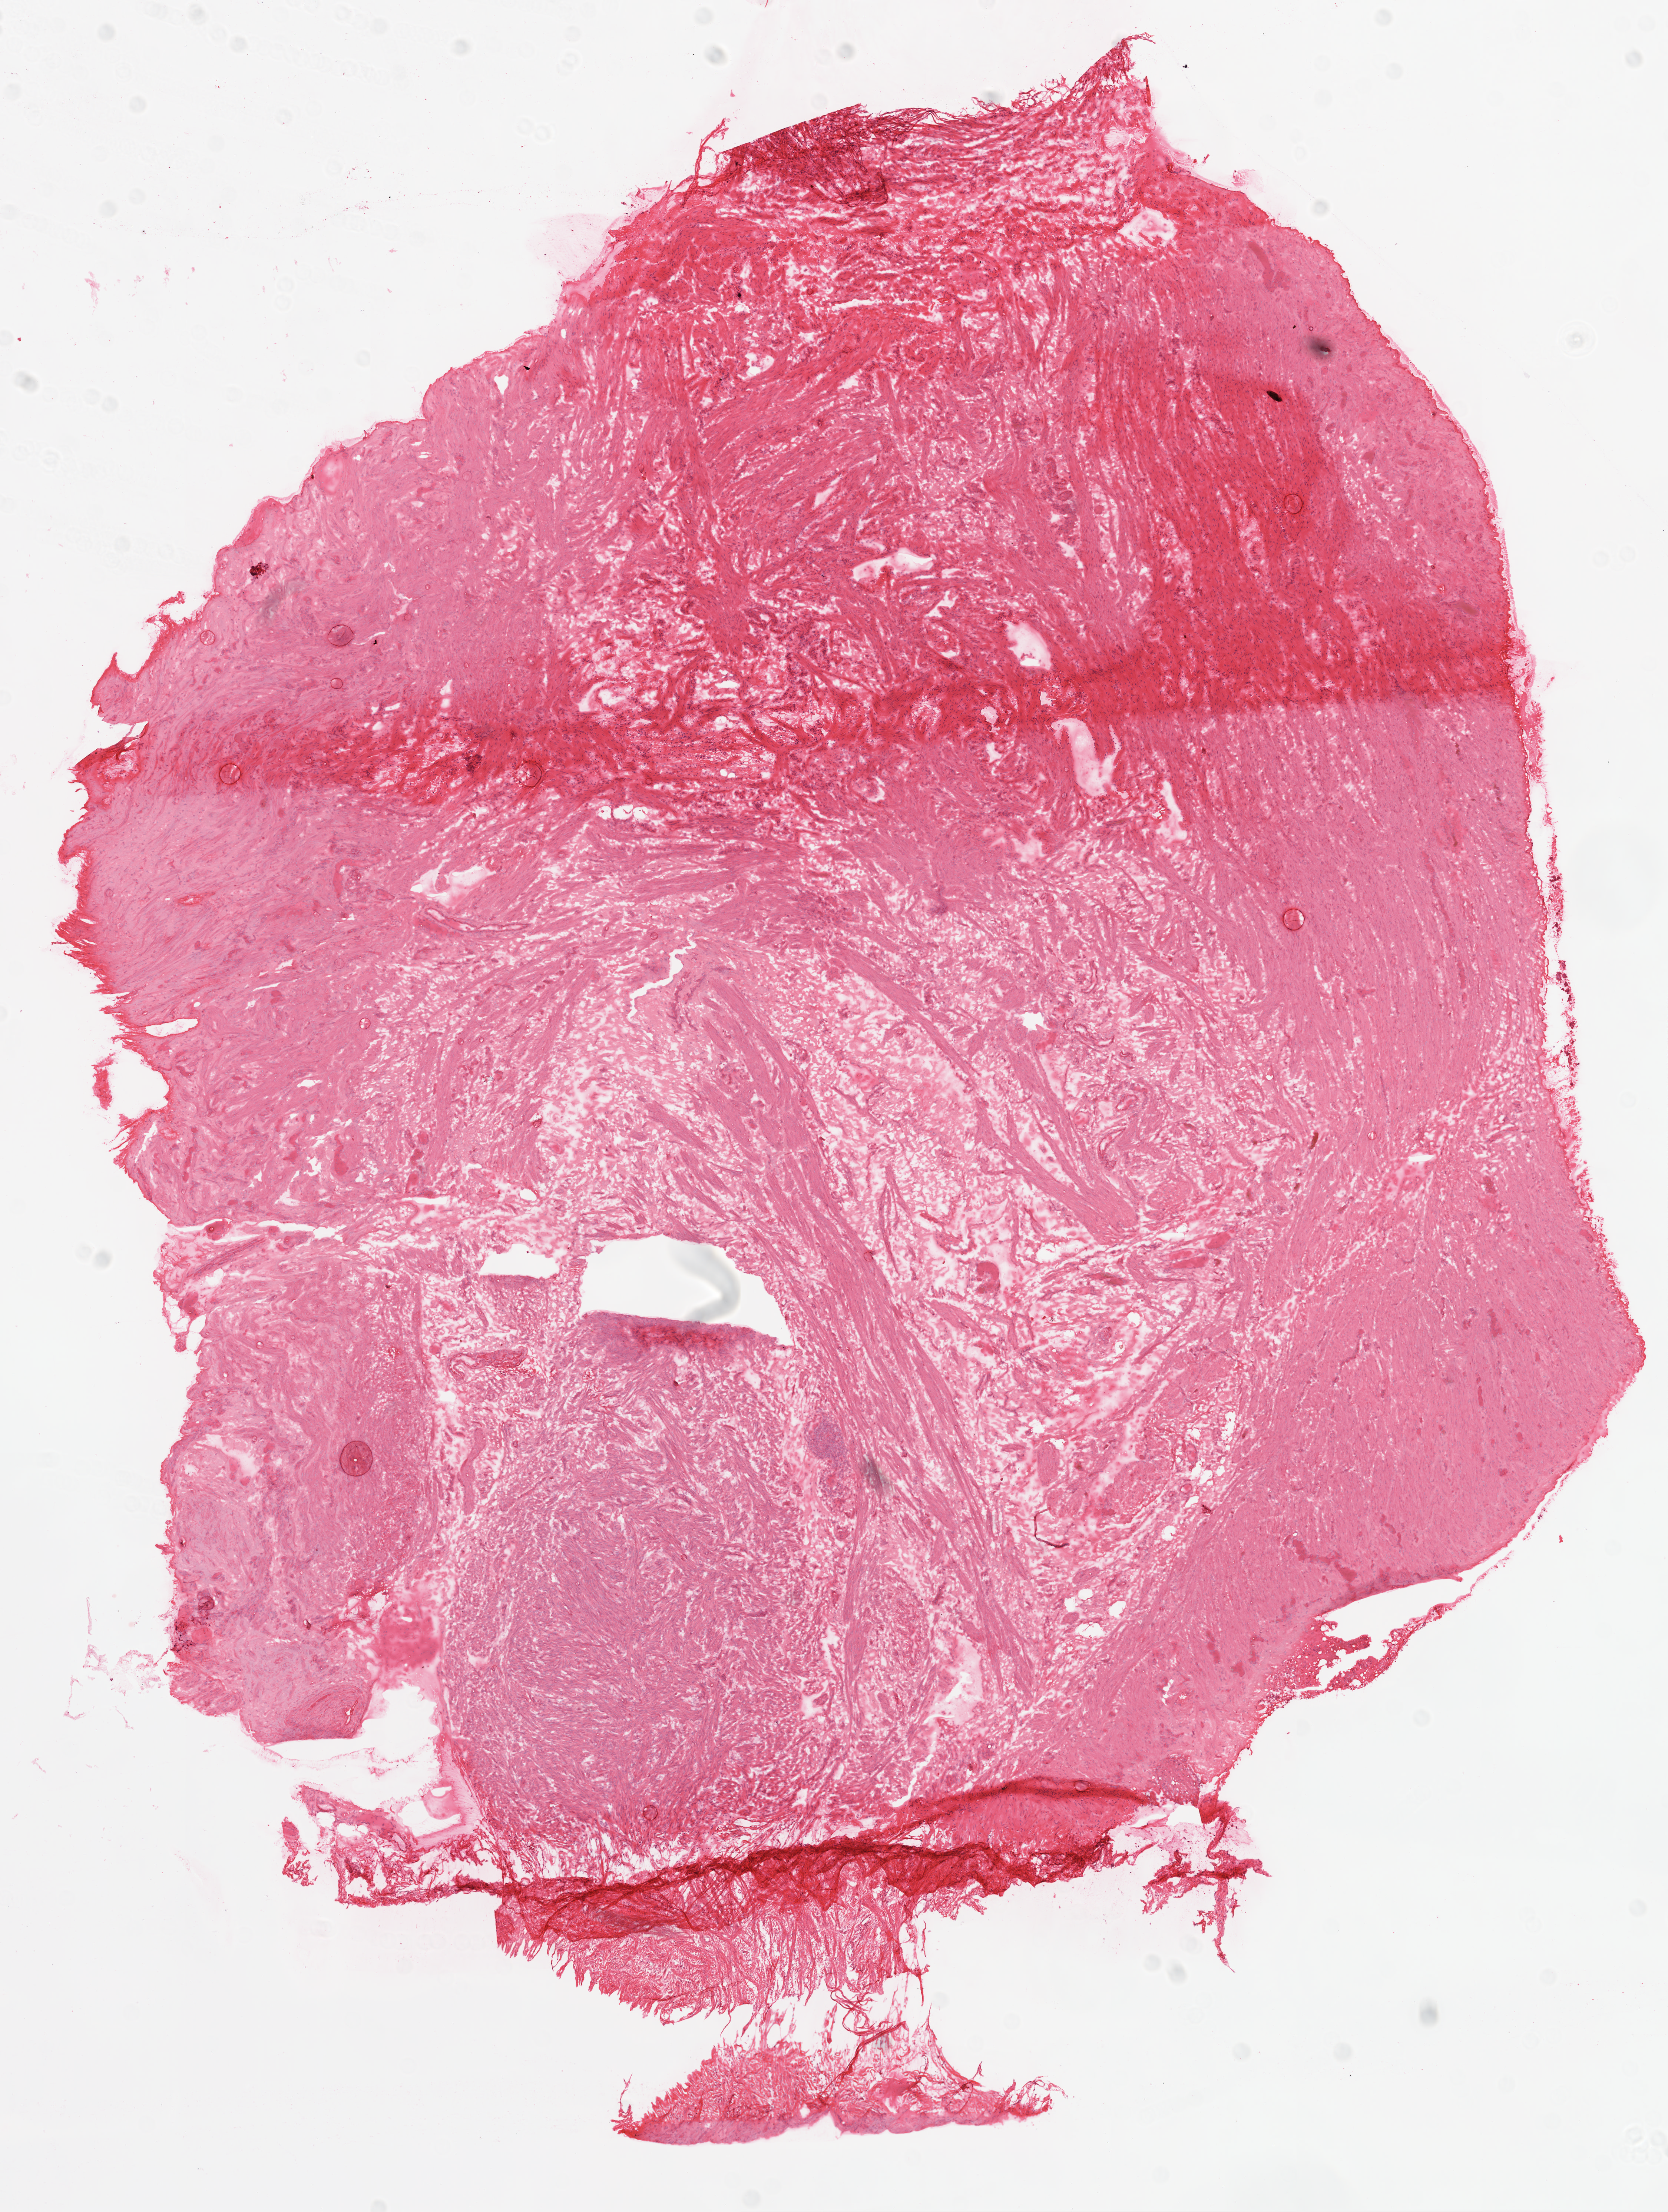
Digitized H&E tissue section (whole slide) — a low-resolution overview of the entire scanned area, about 9.0 x 12.0 mm; frozen section from the top of the tissue portion; ovary, solid tissue normal (non-tumour tissue) sample. Female, age 78 years at initial diagnosis.
• this section: solid tissue normal sample (biorepository sample class)
• patient diagnosis: Serous cystadenocarcinoma, NOS